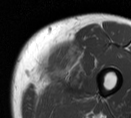
MRI of an extremity soft-tissue mass, one axial slice; slice 15 of 55 in the series (ordered by position); MR volume resampled by the dataset authors to the PET/CT grid (not the native acquisition matrix); 3.27 mm slice thickness; 131 × 118 image matrix, field of view 128 × 115 mm. Male patient. Case-level facts recorded for this patient, not image findings: histological type: pleiomorphic liposarcoma; grade: high; site of the primary tumour: left thigh.
Structures marked on this image (expert contour drawn on MRI and transferred to this co-registered scan by the dataset authors):
- gross tumour volume including surrounding oedema: bounding box (x1, y1, x2, y2) in pixels: (32, 45, 94, 99)
- gross tumour volume (mass): (32, 45, 67, 88)